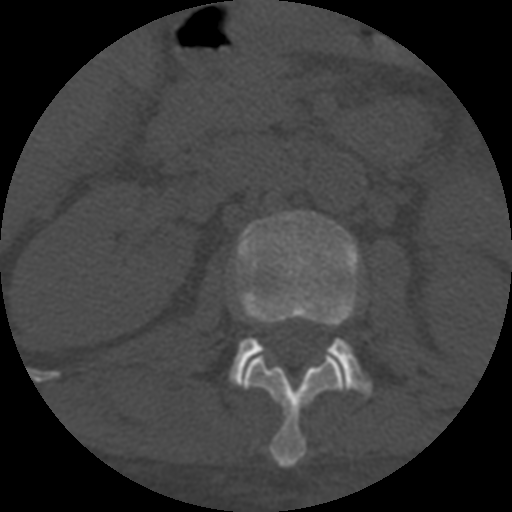
CT including the spine, one axial slice. Position 273 of 708 along the scan axis. 120 kVp. One of 3 acquisitions stored at this slice position. Bone window (W 1800 / L 400 HU). 1.25 mm slice thickness. 512 × 512 image matrix. Patient age 55 years. From the clinical record (not read from this slice): primary cancer: colon; vertebrae with lytic lesions (as recorded): T12, L1, L5.
Outlined on this slice (semi-automatic segmentation, software-assisted and operator-edited):
- L1 vertebra: bounding box [x1, y1, x2, y2] px = [243, 350, 348, 467]
- L2 vertebra: [230, 210, 370, 395]